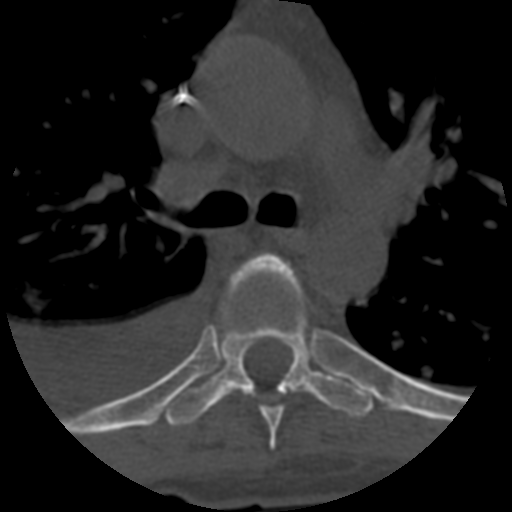
CT including the spine, one axial slice. Slice 443 of 708 in the series (ordered by position). Reconstruction kernel STANDARD. 120 kVp. One of 3 acquisitions stored at this slice position. Bone window (W 1800 / L 400 HU). 1.25 mm slice thickness. 512 × 512 image matrix, field of view 160 × 160 mm. Patient age 55 years. From the clinical record (not read from this slice): primary cancer: colon; vertebrae with lytic lesions (as recorded): T12, L1, L5.
Outlined on this slice (semi-automatic segmentation, software-assisted and operator-edited):
- T5 vertebra: box from (x=231, y=255) to (x=283, y=450) px
- T6 vertebra: (x=165, y=253)–(x=374, y=427)